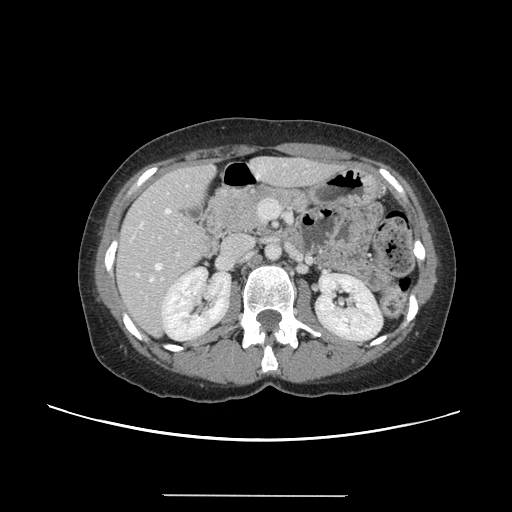
Contrast-enhanced abdominal CT, one axial slice; slice 66 of 144 in the series (ordered by position); 120 kVp; intravenous contrast given; soft-tissue window (W 400 / L 40 HU); 512 × 512 image matrix, field of view 380 × 380 mm. Female patient, age 53 years. Case-level facts recorded for this patient, not image findings: diagnosis: colorectal cancer liver metastases, imaged before liver resection; multiple liver metastases: yes; largest metastasis: 1.1 cm; disease in both lobes: no.
Annotated regions visible in this slice (manually delineated by an expert):
- hepatic veins: bounding box (x1, y1, x2, y2) in pixels: (137, 185, 188, 282)
- liver: (119, 159, 336, 334)
- planned liver remnant (the part of the liver to remain after resection): (119, 159, 325, 306)
- portal vein (with intrahepatic branches): (161, 199, 281, 281)